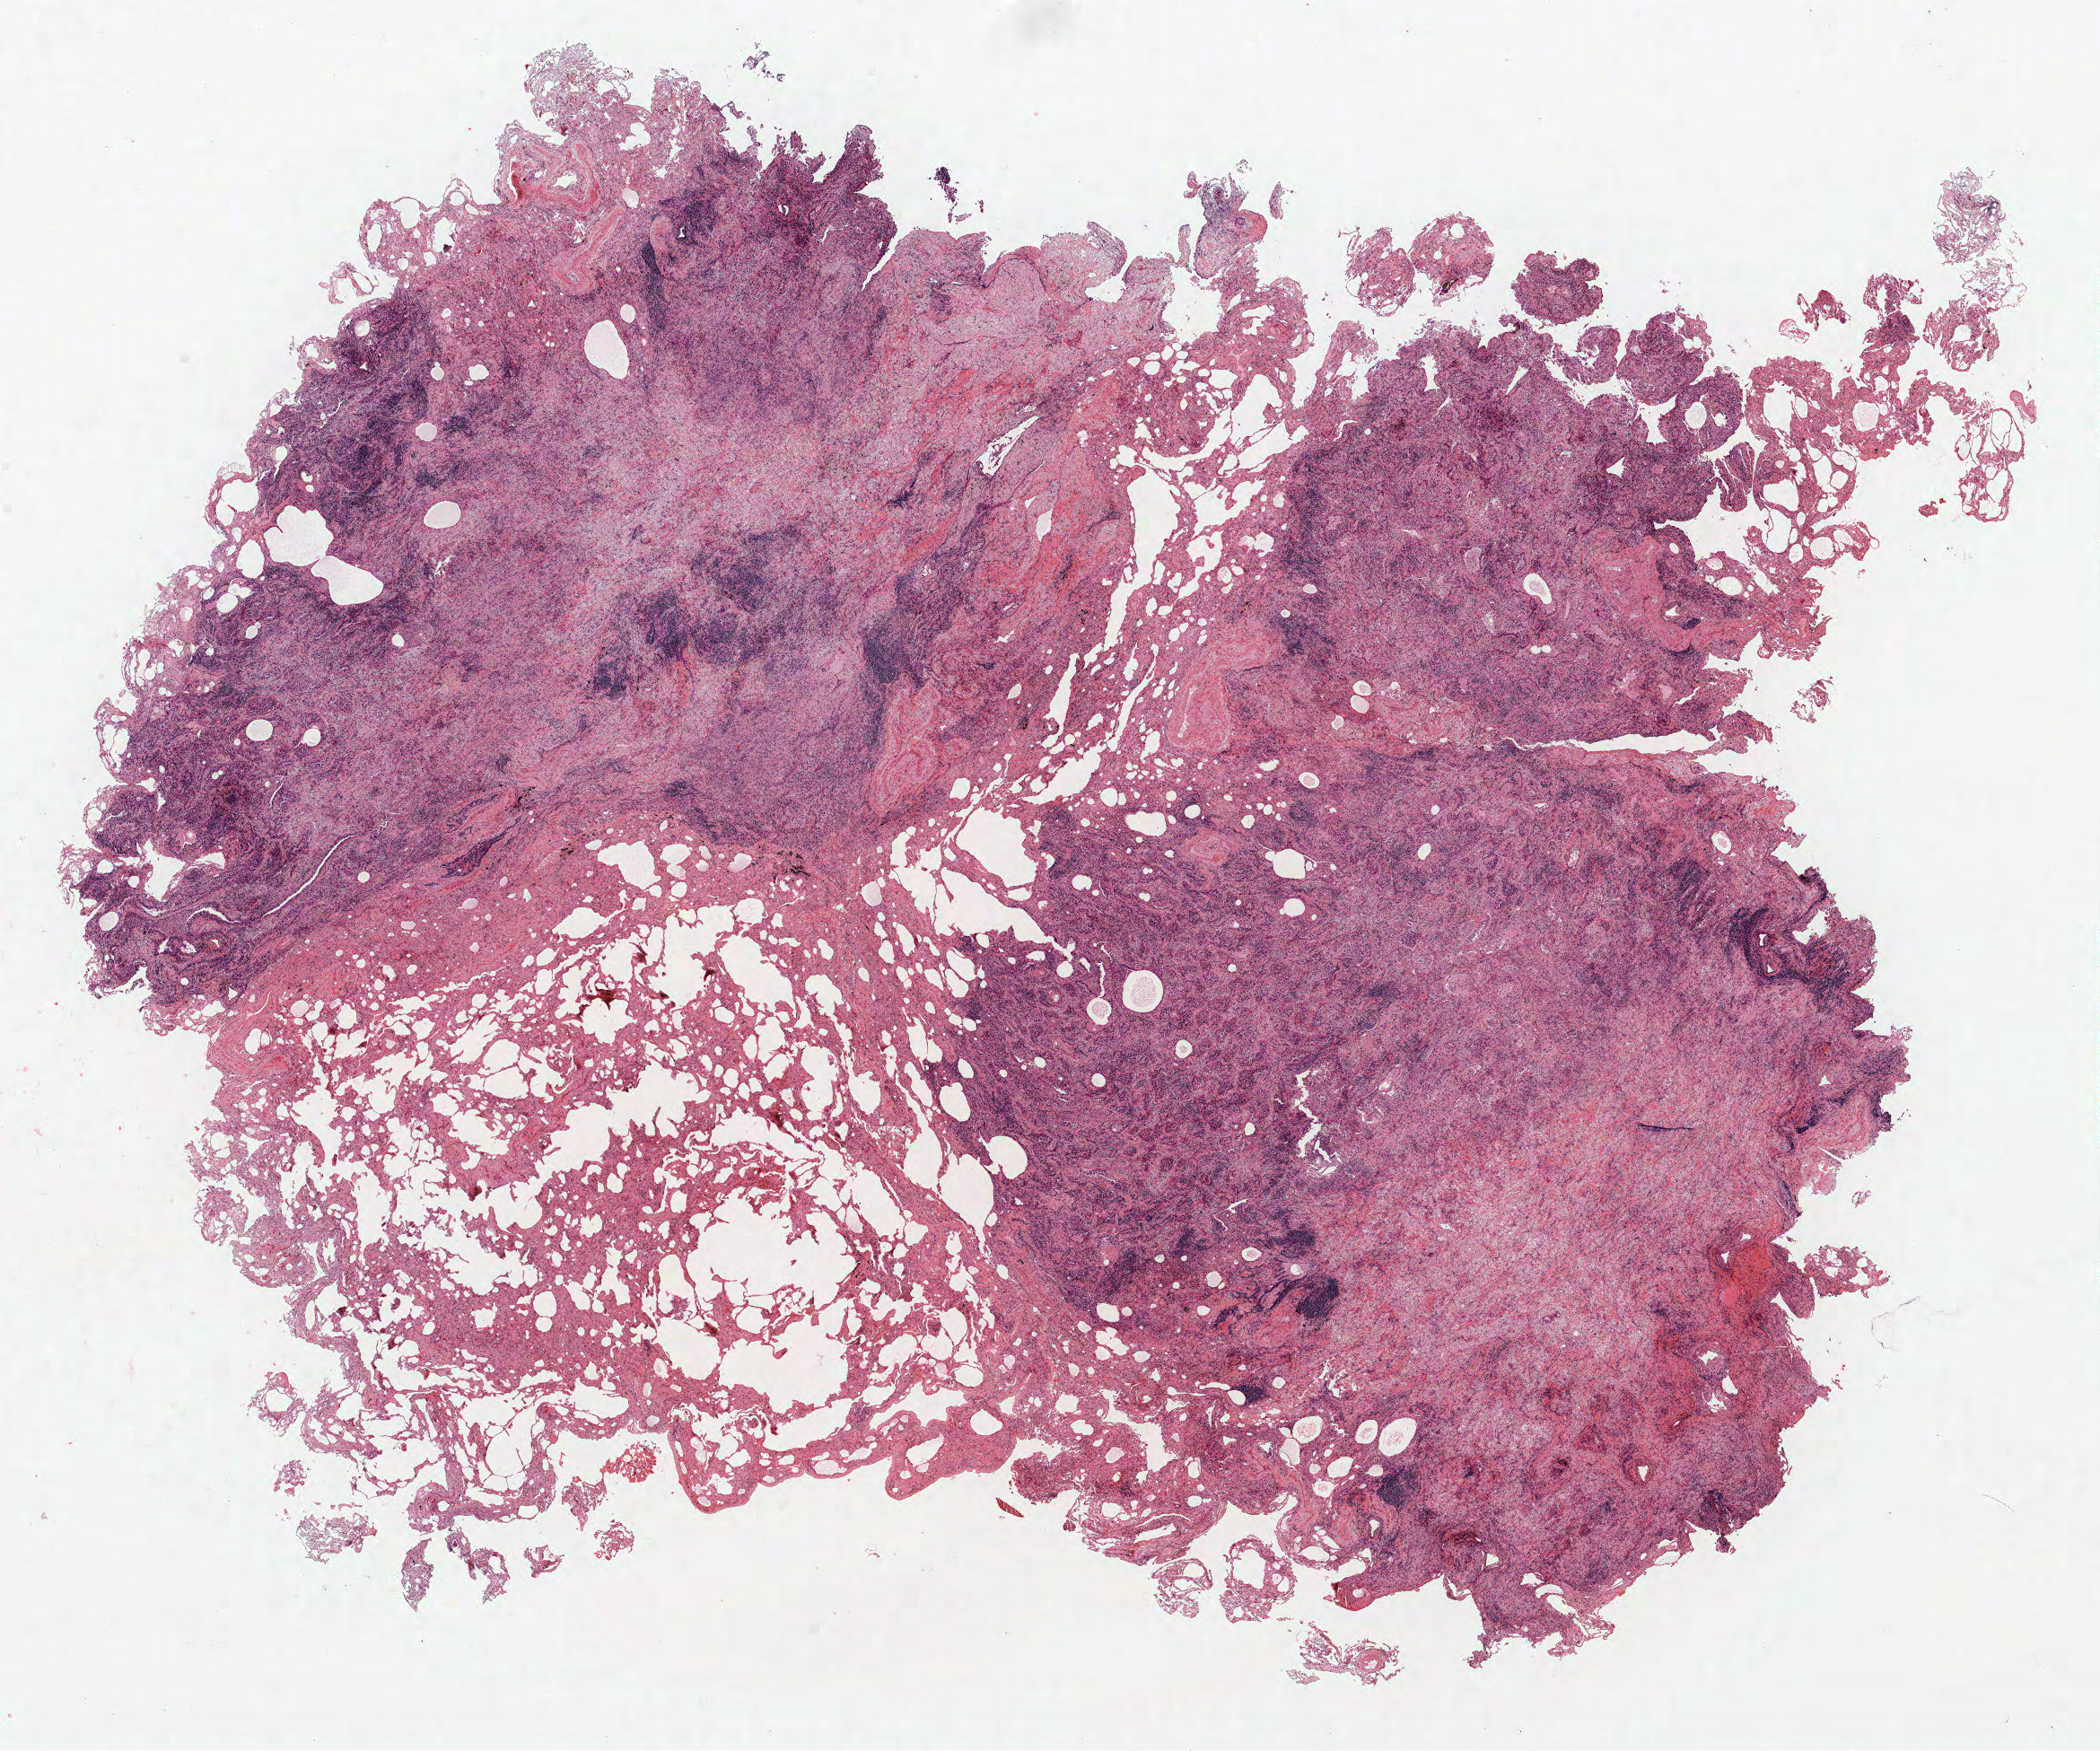
Whole-slide histology image, H&E-stained, shown as a low-resolution overview of the whole scanned area (about 18.7 x 15.6 mm, from a 40x scan); FFPE section; lung. Female, age 73 at enrolment. Grade: moderately differentiated (G2).
* ICD-O-3 topography: upper lobe of lung (C34.1)
* primary tumour location (clinical record): left upper lobe
* stage (AJCC 6th edition): IIIB
* tumour size (pathology): 17 mm
* participant's lung-cancer diagnosis: Bronchiolo-alveolar adenocarcinoma, NOS